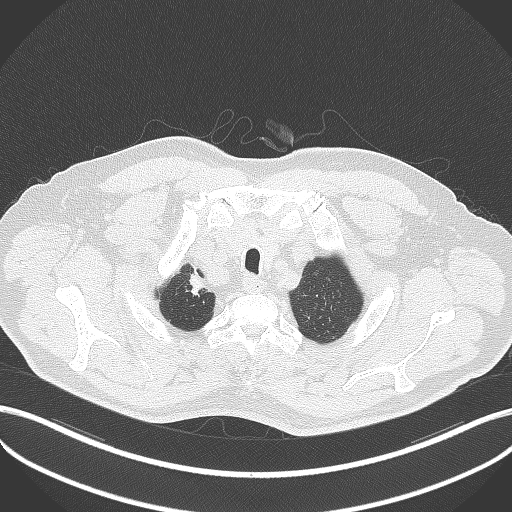
Chest CT, one axial slice. Position 349 of 411 along the scan axis. Reconstruction kernel B70f. 120 kVp. Lung window (W 1500 / L -600 HU). 1 mm slice thickness. 512 × 512 image matrix, field of view 400 × 400 mm. Male patient, age 60 years. Case-level facts recorded for this patient, not image findings: clinical TNM (as recorded): T1b N1 M0.
Outlined on this slice (bounding box drawn by a radiologist):
- lung tumour (recorded histology: squamous cell carcinoma): bounding box (x1, y1, x2, y2) in pixels: (188, 271, 205, 297)